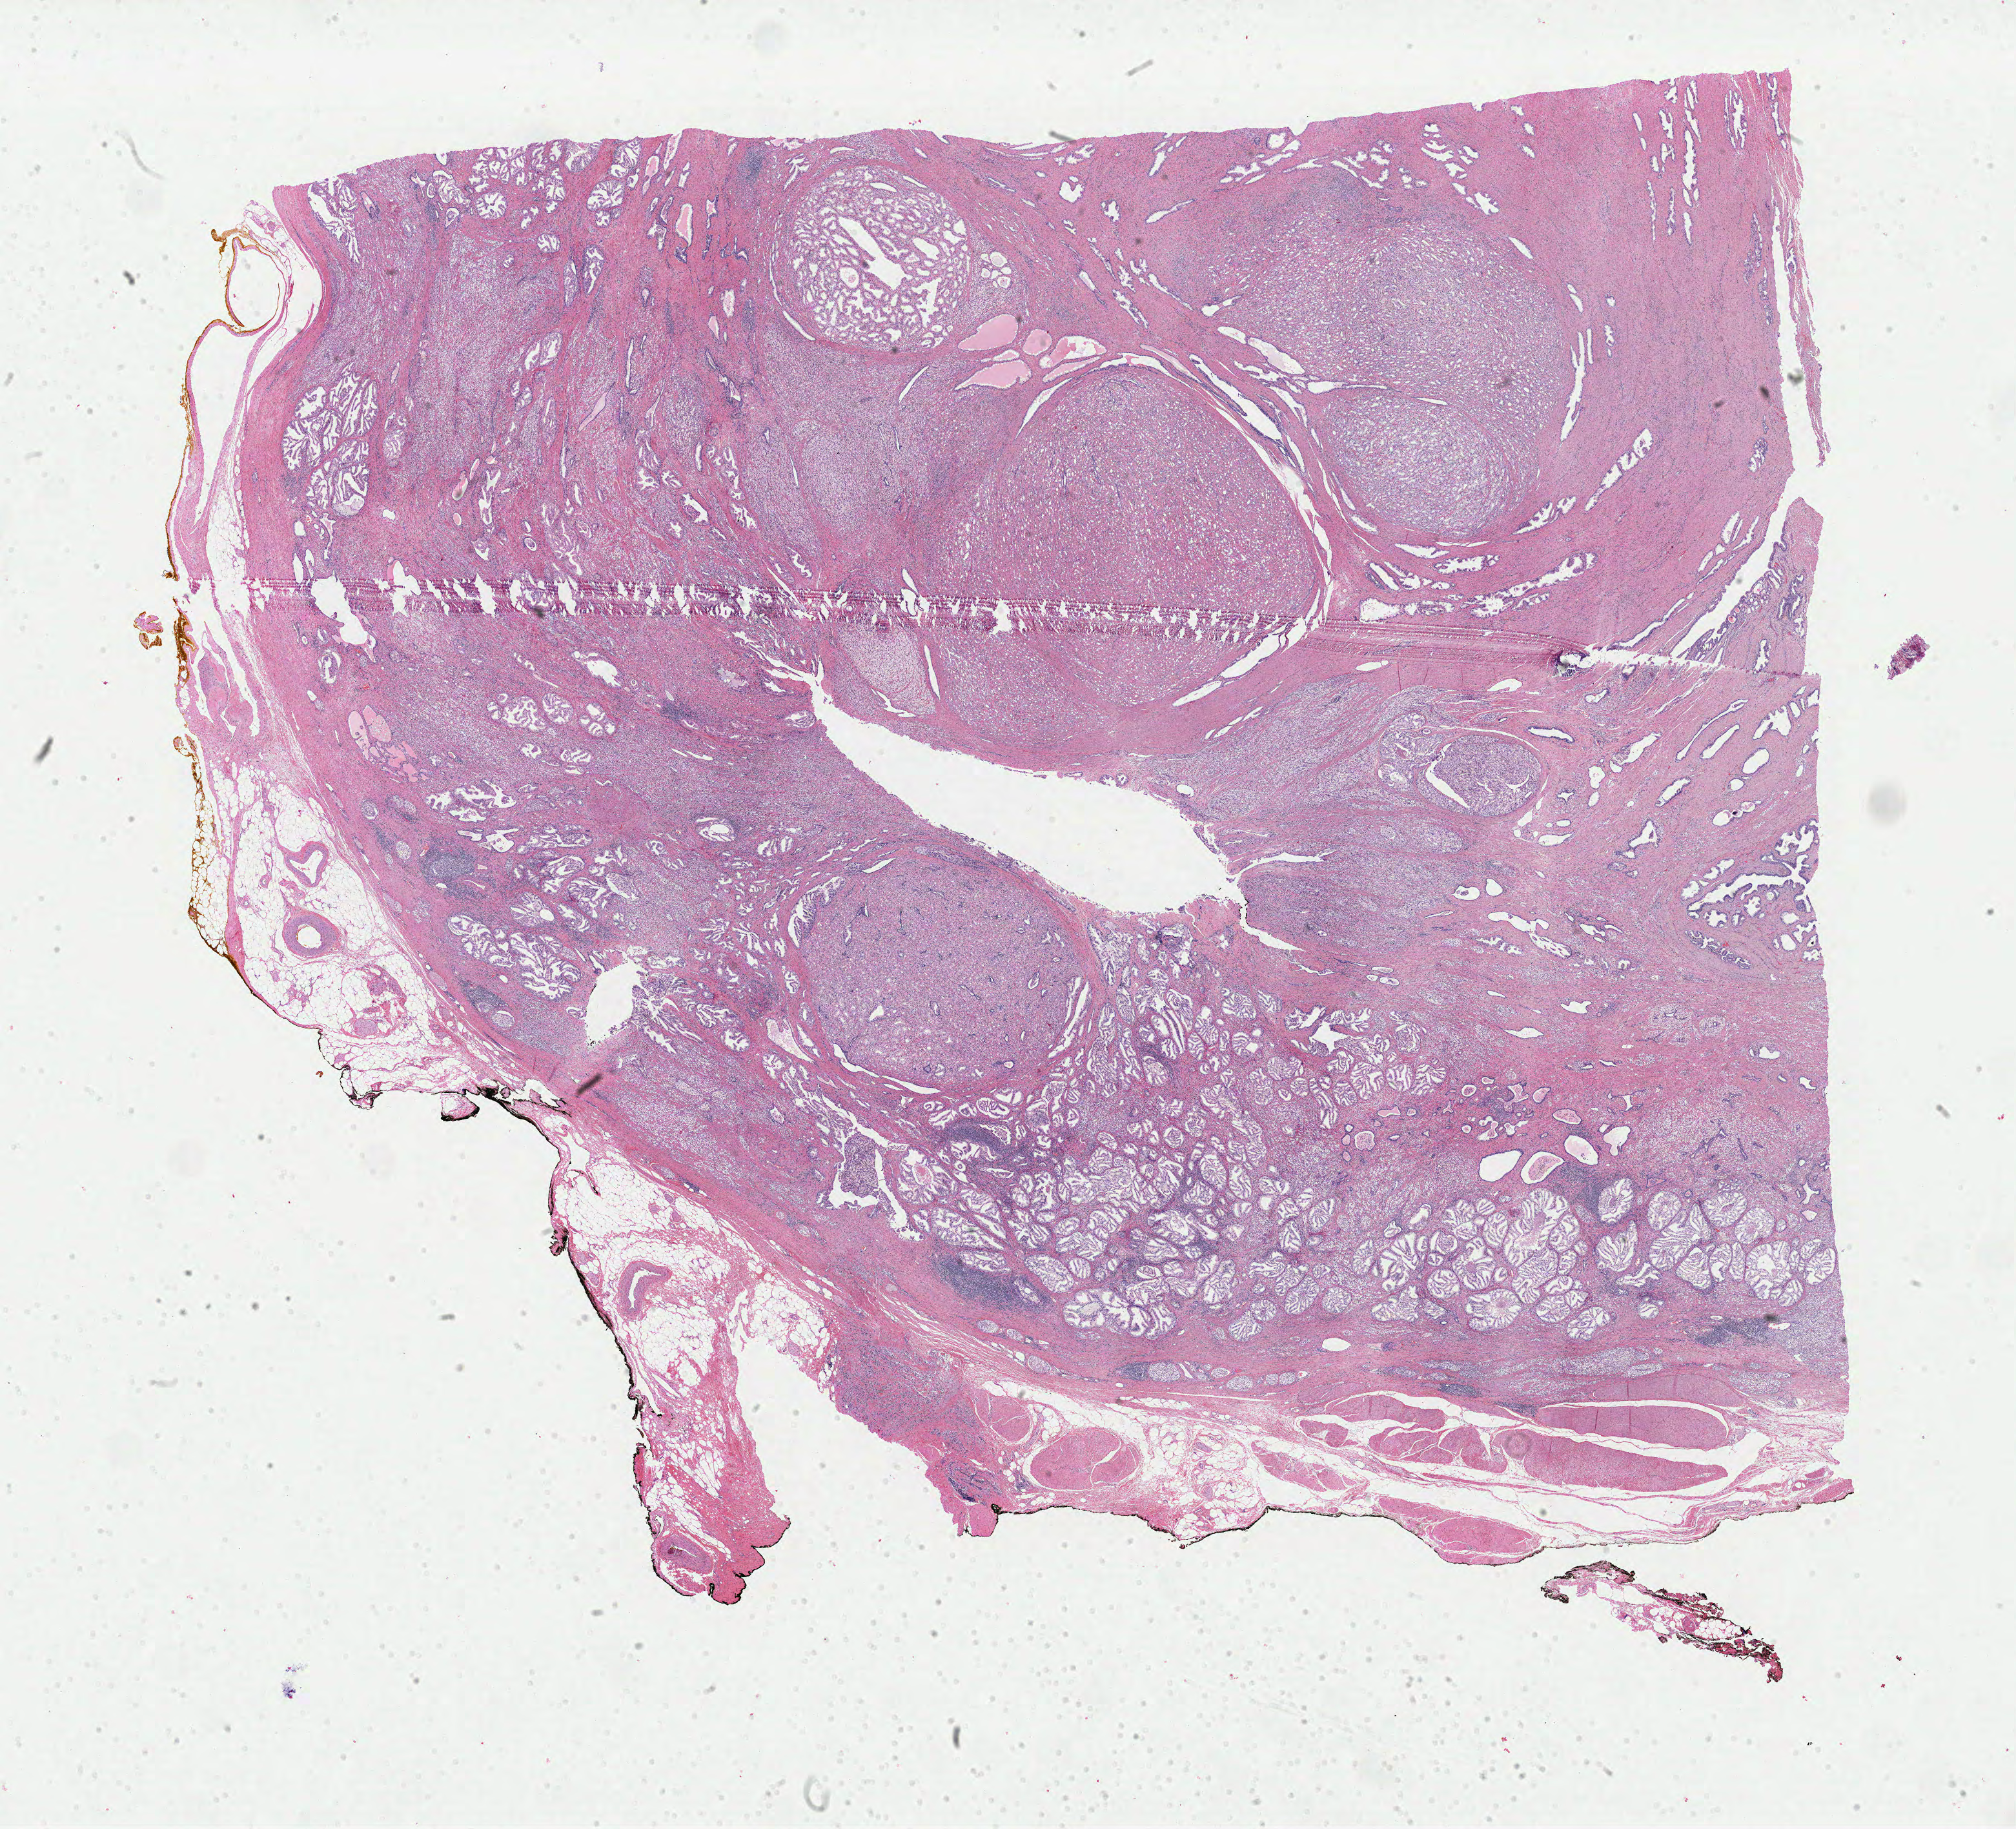
Digitized H&E-stained tissue section (whole slide), low-resolution overview of the scanned area, about 24.7 x 22.4 mm, FFPE section, prostate, primary tumour sample. Male patient; age at initial diagnosis 55 years. Gleason score: 9 (5+4).
* diagnosis: Adenocarcinoma, NOS (prostate gland)
* laterality: bilateral